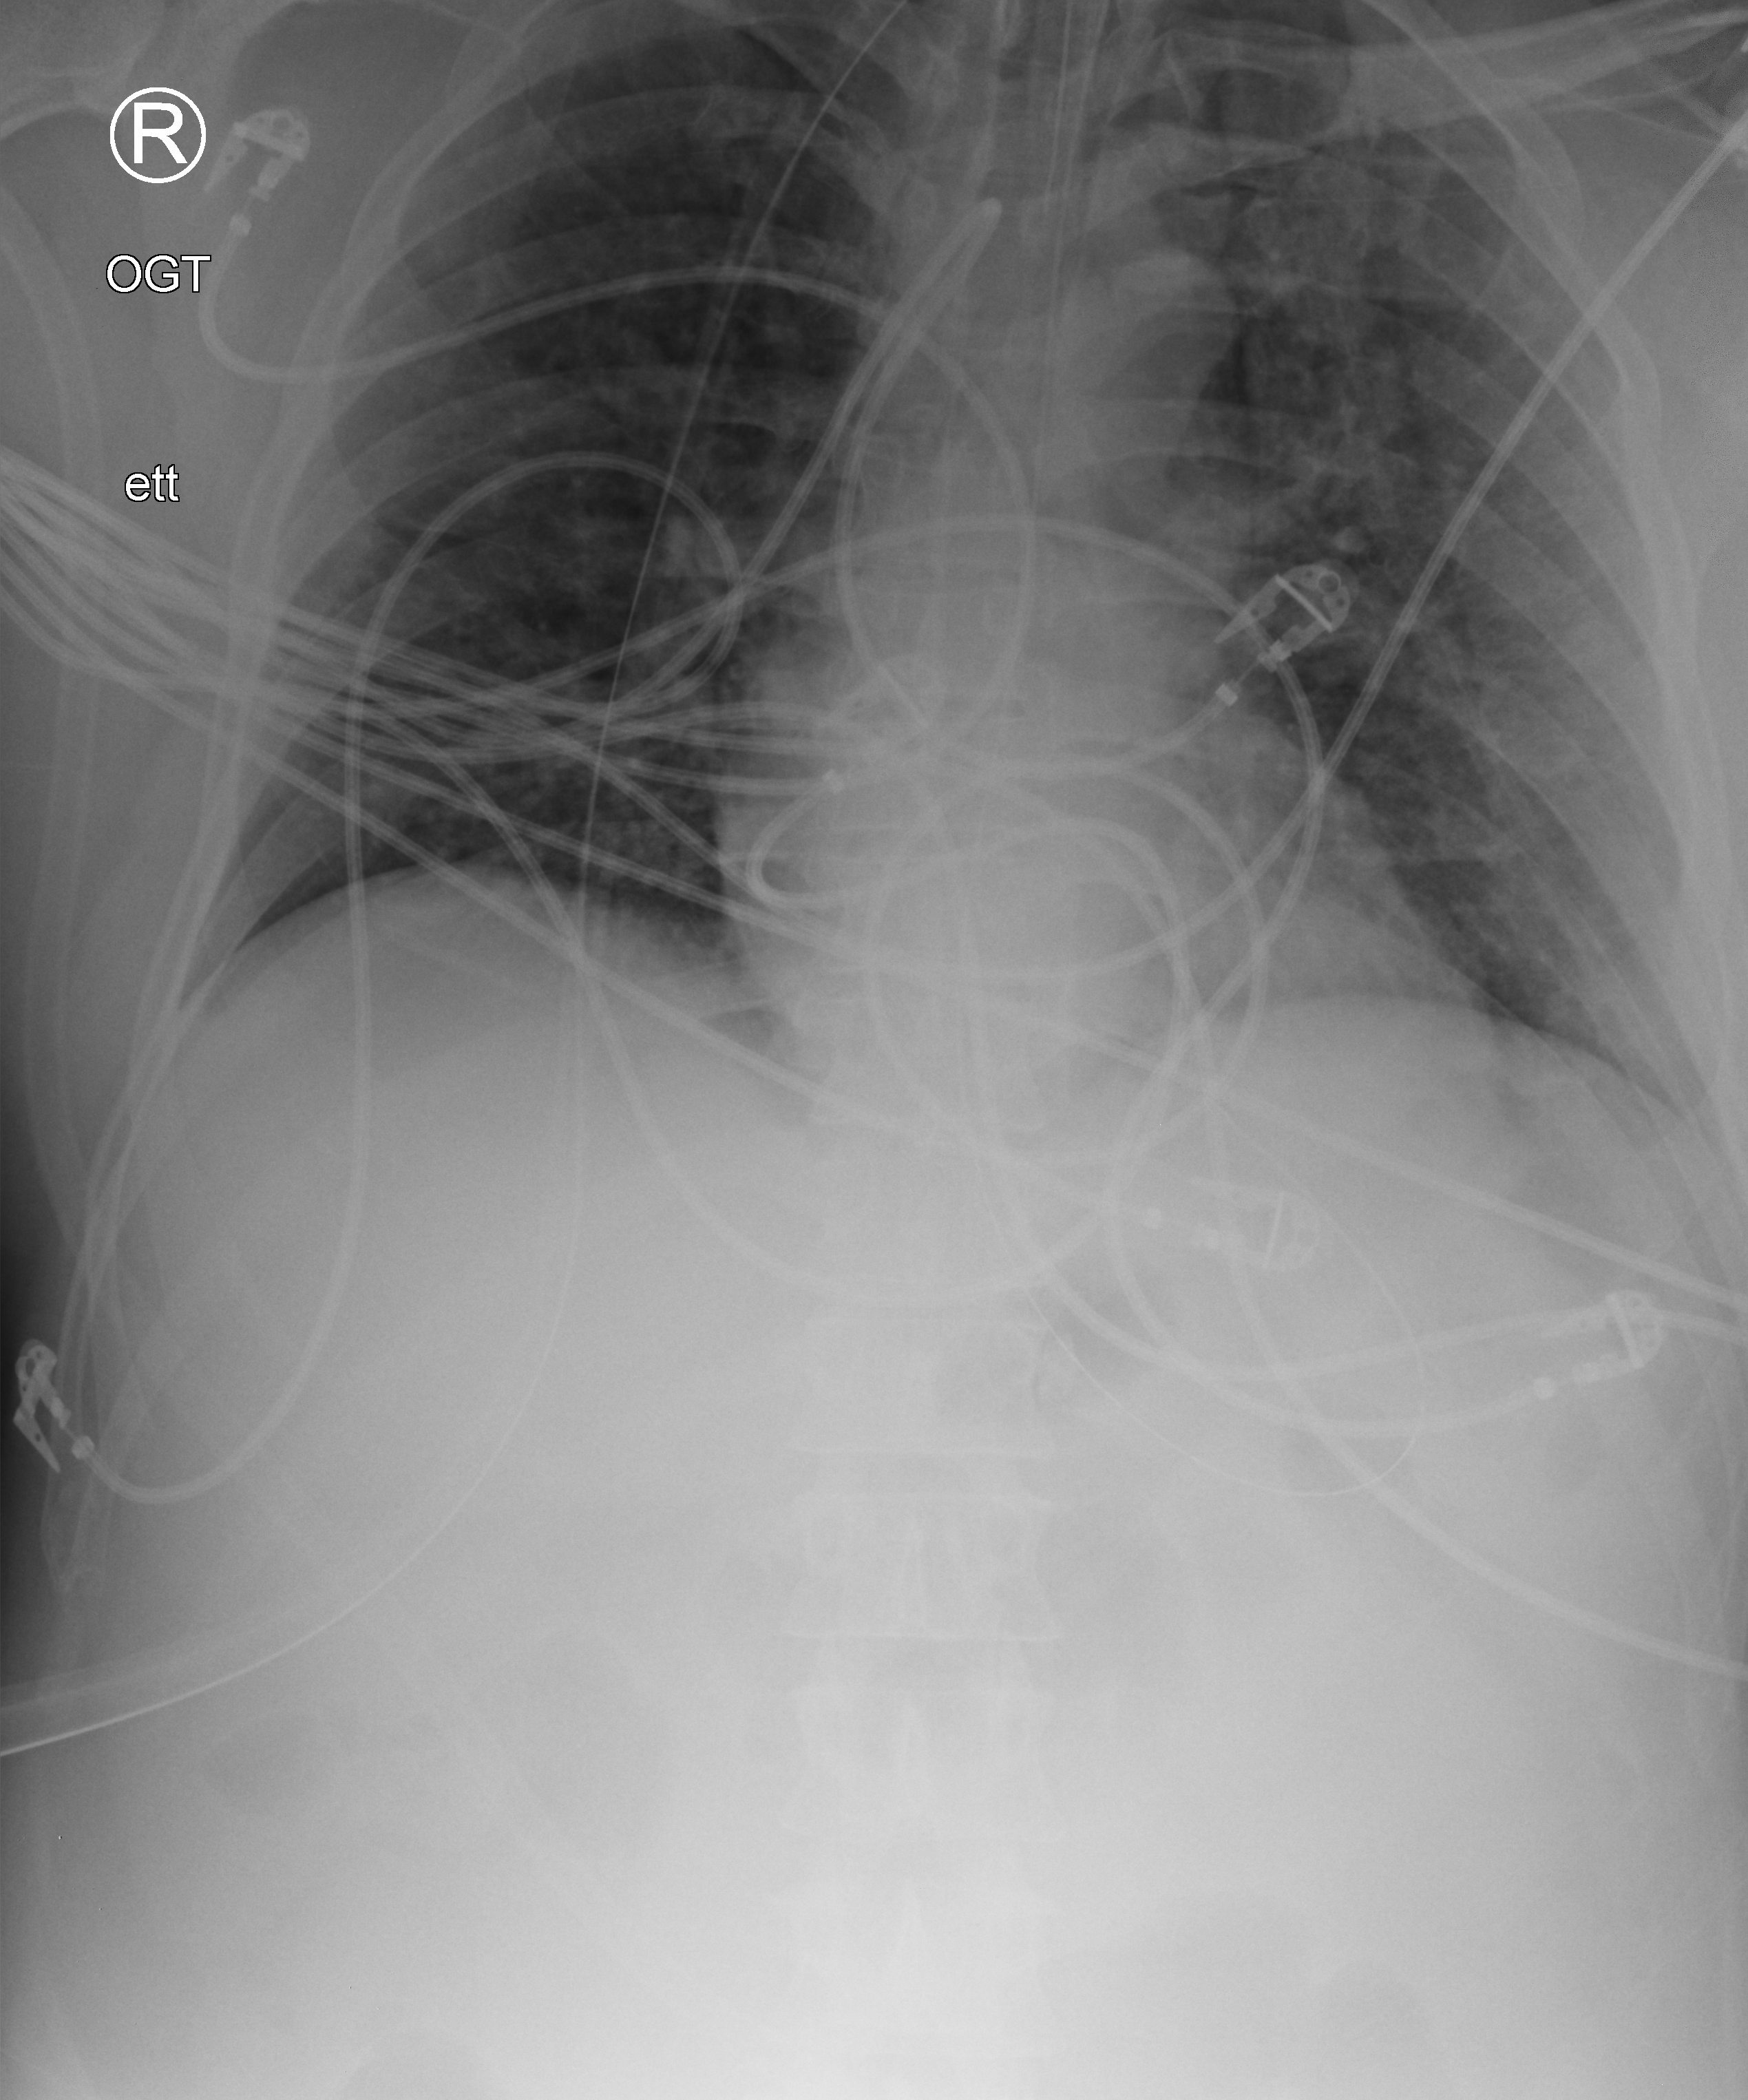
Portable chest radiograph. Male patient hospitalised with COVID-19, age 18–59 years.
From the hospital-stay record, not from the radiograph (when in the stay this image was taken is not recorded): mechanically ventilated during this hospital stay: yes; admitted to intensive care during this hospital stay: yes; diabetes (admission record): no.